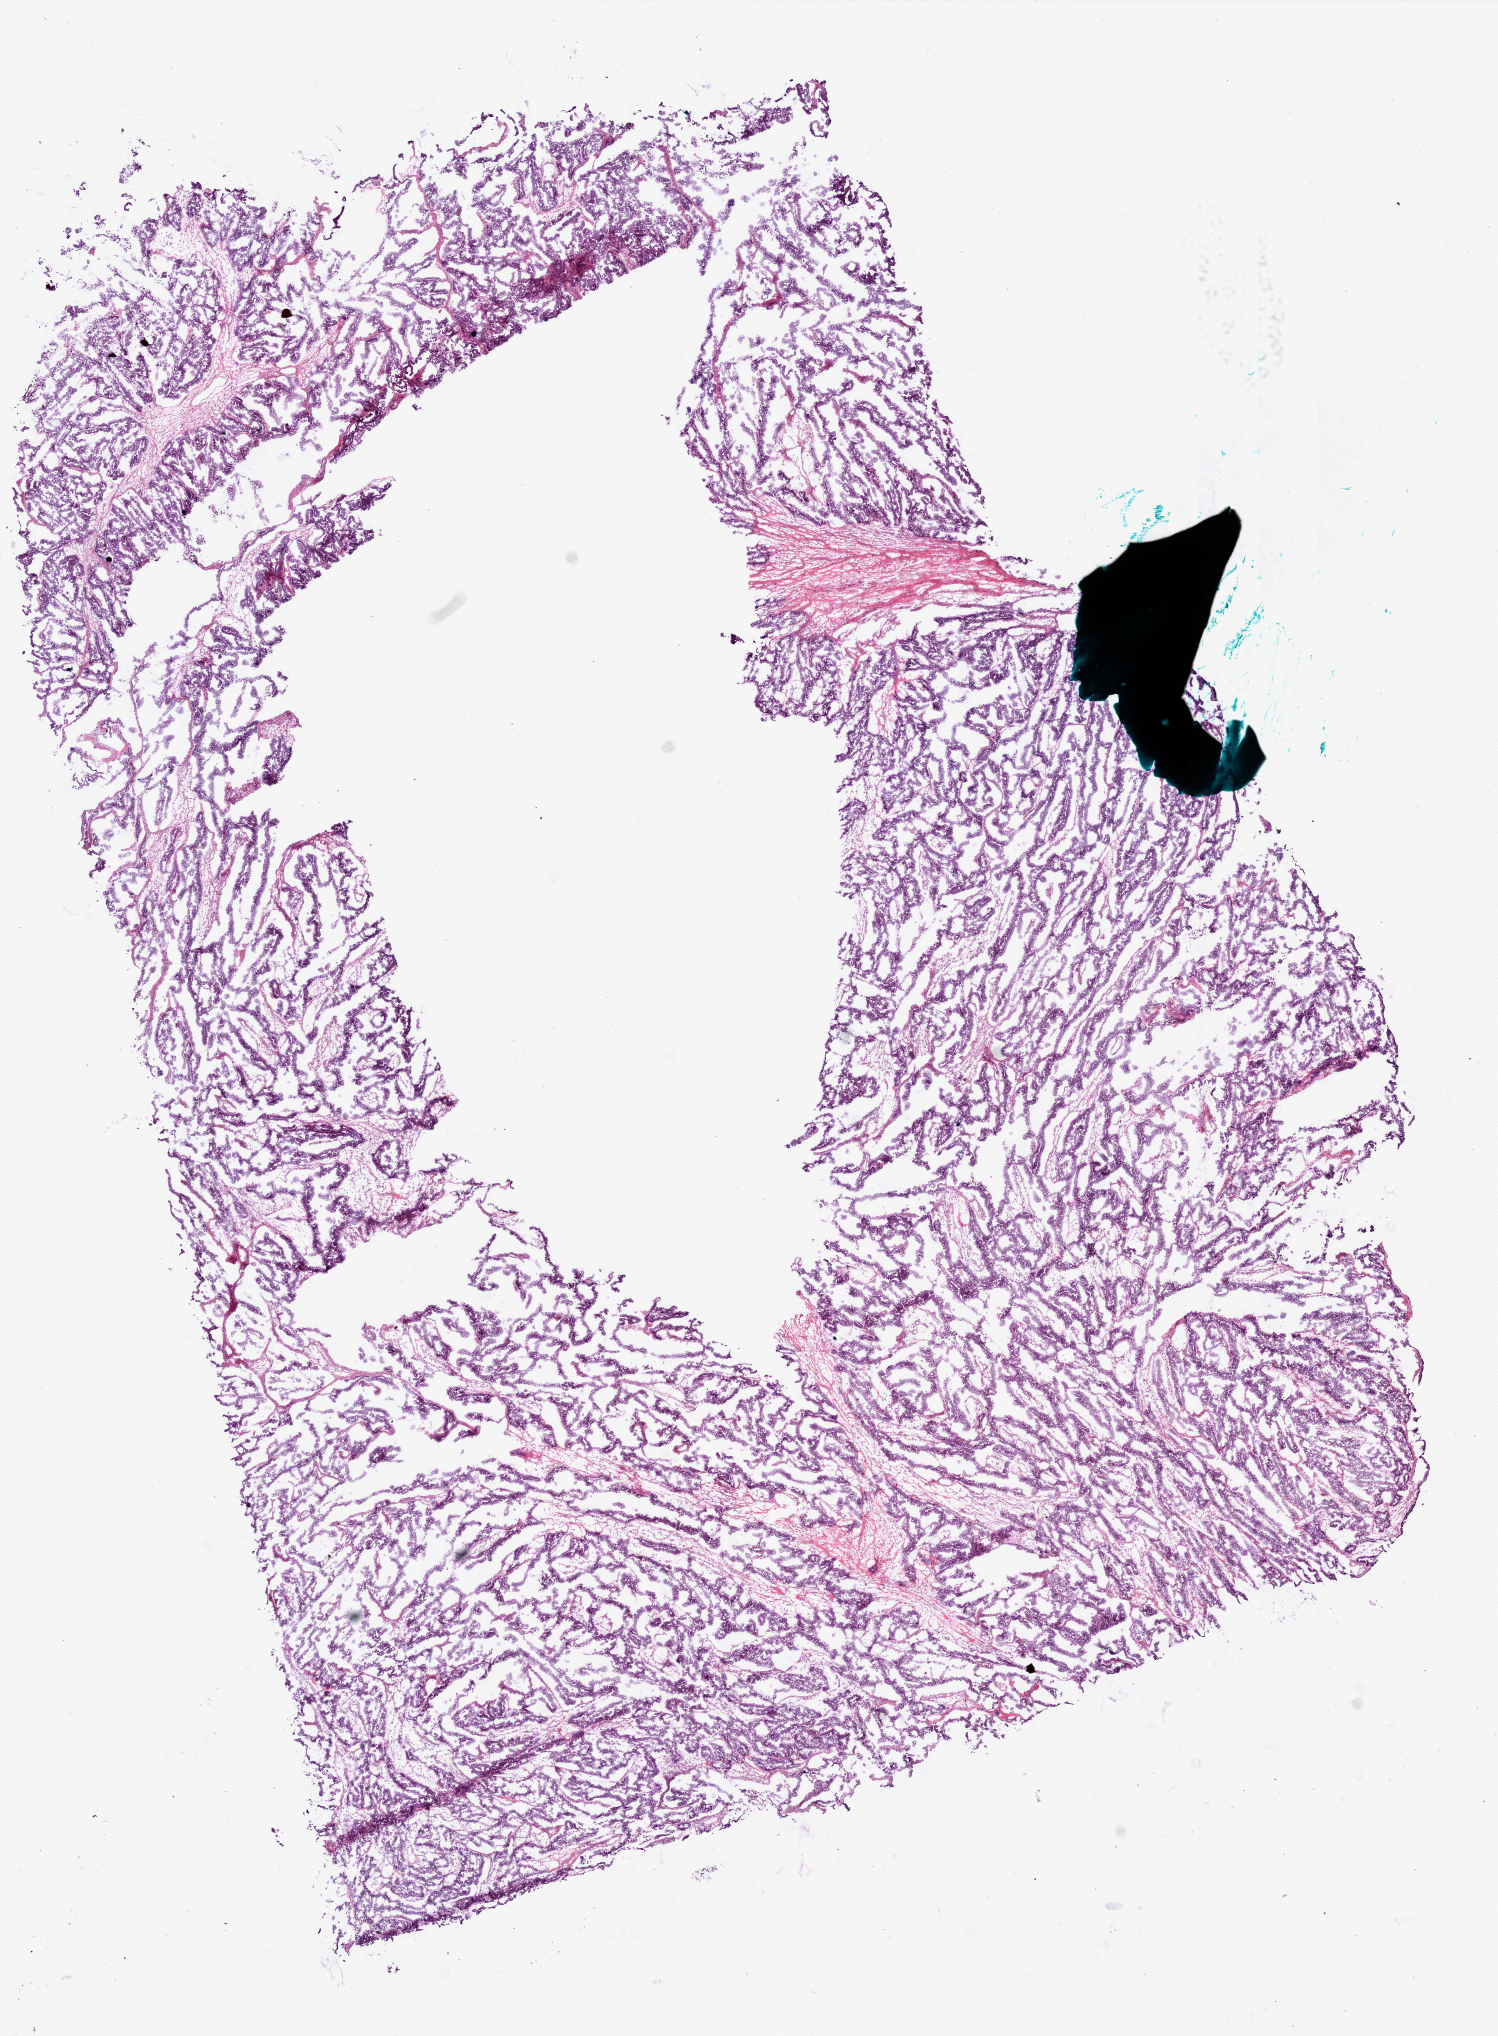
Digitized H&E tissue section (whole slide) — shown as a low-resolution overview of the whole scanned area (about 12.0 x 16.4 mm); frozen section from the bottom of the tissue portion; ovary, primary tumour sample. Female, age 79 years at initial diagnosis. Histologic grade: G3 (poorly differentiated). Composition of this section per pathologist review: tumour cells 80%, tumour nuclei 85%, normal cells 0%, stromal cells 20%, necrosis 0%.
• FIGO stage: IIIC
• laterality: bilateral
• diagnosis: Serous cystadenocarcinoma, NOS